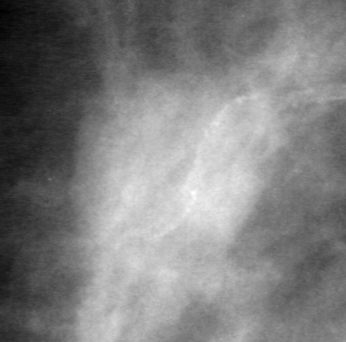
Region of interest cut from a scanned film mammogram (one marked finding); right breast; MLO view.
Finding: mass, shape round, margins obscured; BI-RADS assessment category 0 (incomplete: needs additional imaging); subtlety rating 4 on a 1 (subtle) to 5 (obvious) scale; pathology result (as recorded, not read from the image): benign.